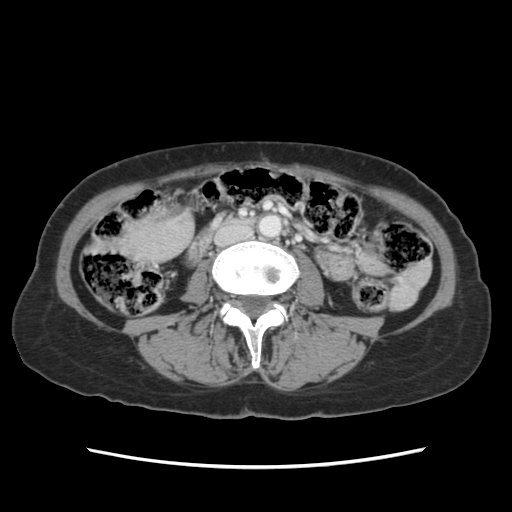
Contrast-enhanced abdominal CT, one axial slice; slice 15 of 120 in the series (ordered by position); 120 kVp; intravenous contrast given; soft-tissue window (W 400 / L 40 HU); 2.5 mm slice thickness; 512 × 512 image matrix. Female patient, age 70 years. Case-level facts recorded for this patient, not image findings: diagnosis: colorectal cancer liver metastases, imaged before liver resection; multiple liver metastases: no; largest metastasis: 2.5 cm; disease in both lobes: no.
Outlined on this slice (outlined manually by an expert reader):
- liver: bounding box [x1, y1, x2, y2] px = [124, 212, 189, 258]
- planned liver remnant (the part of the liver to remain after resection): [124, 213, 190, 258]